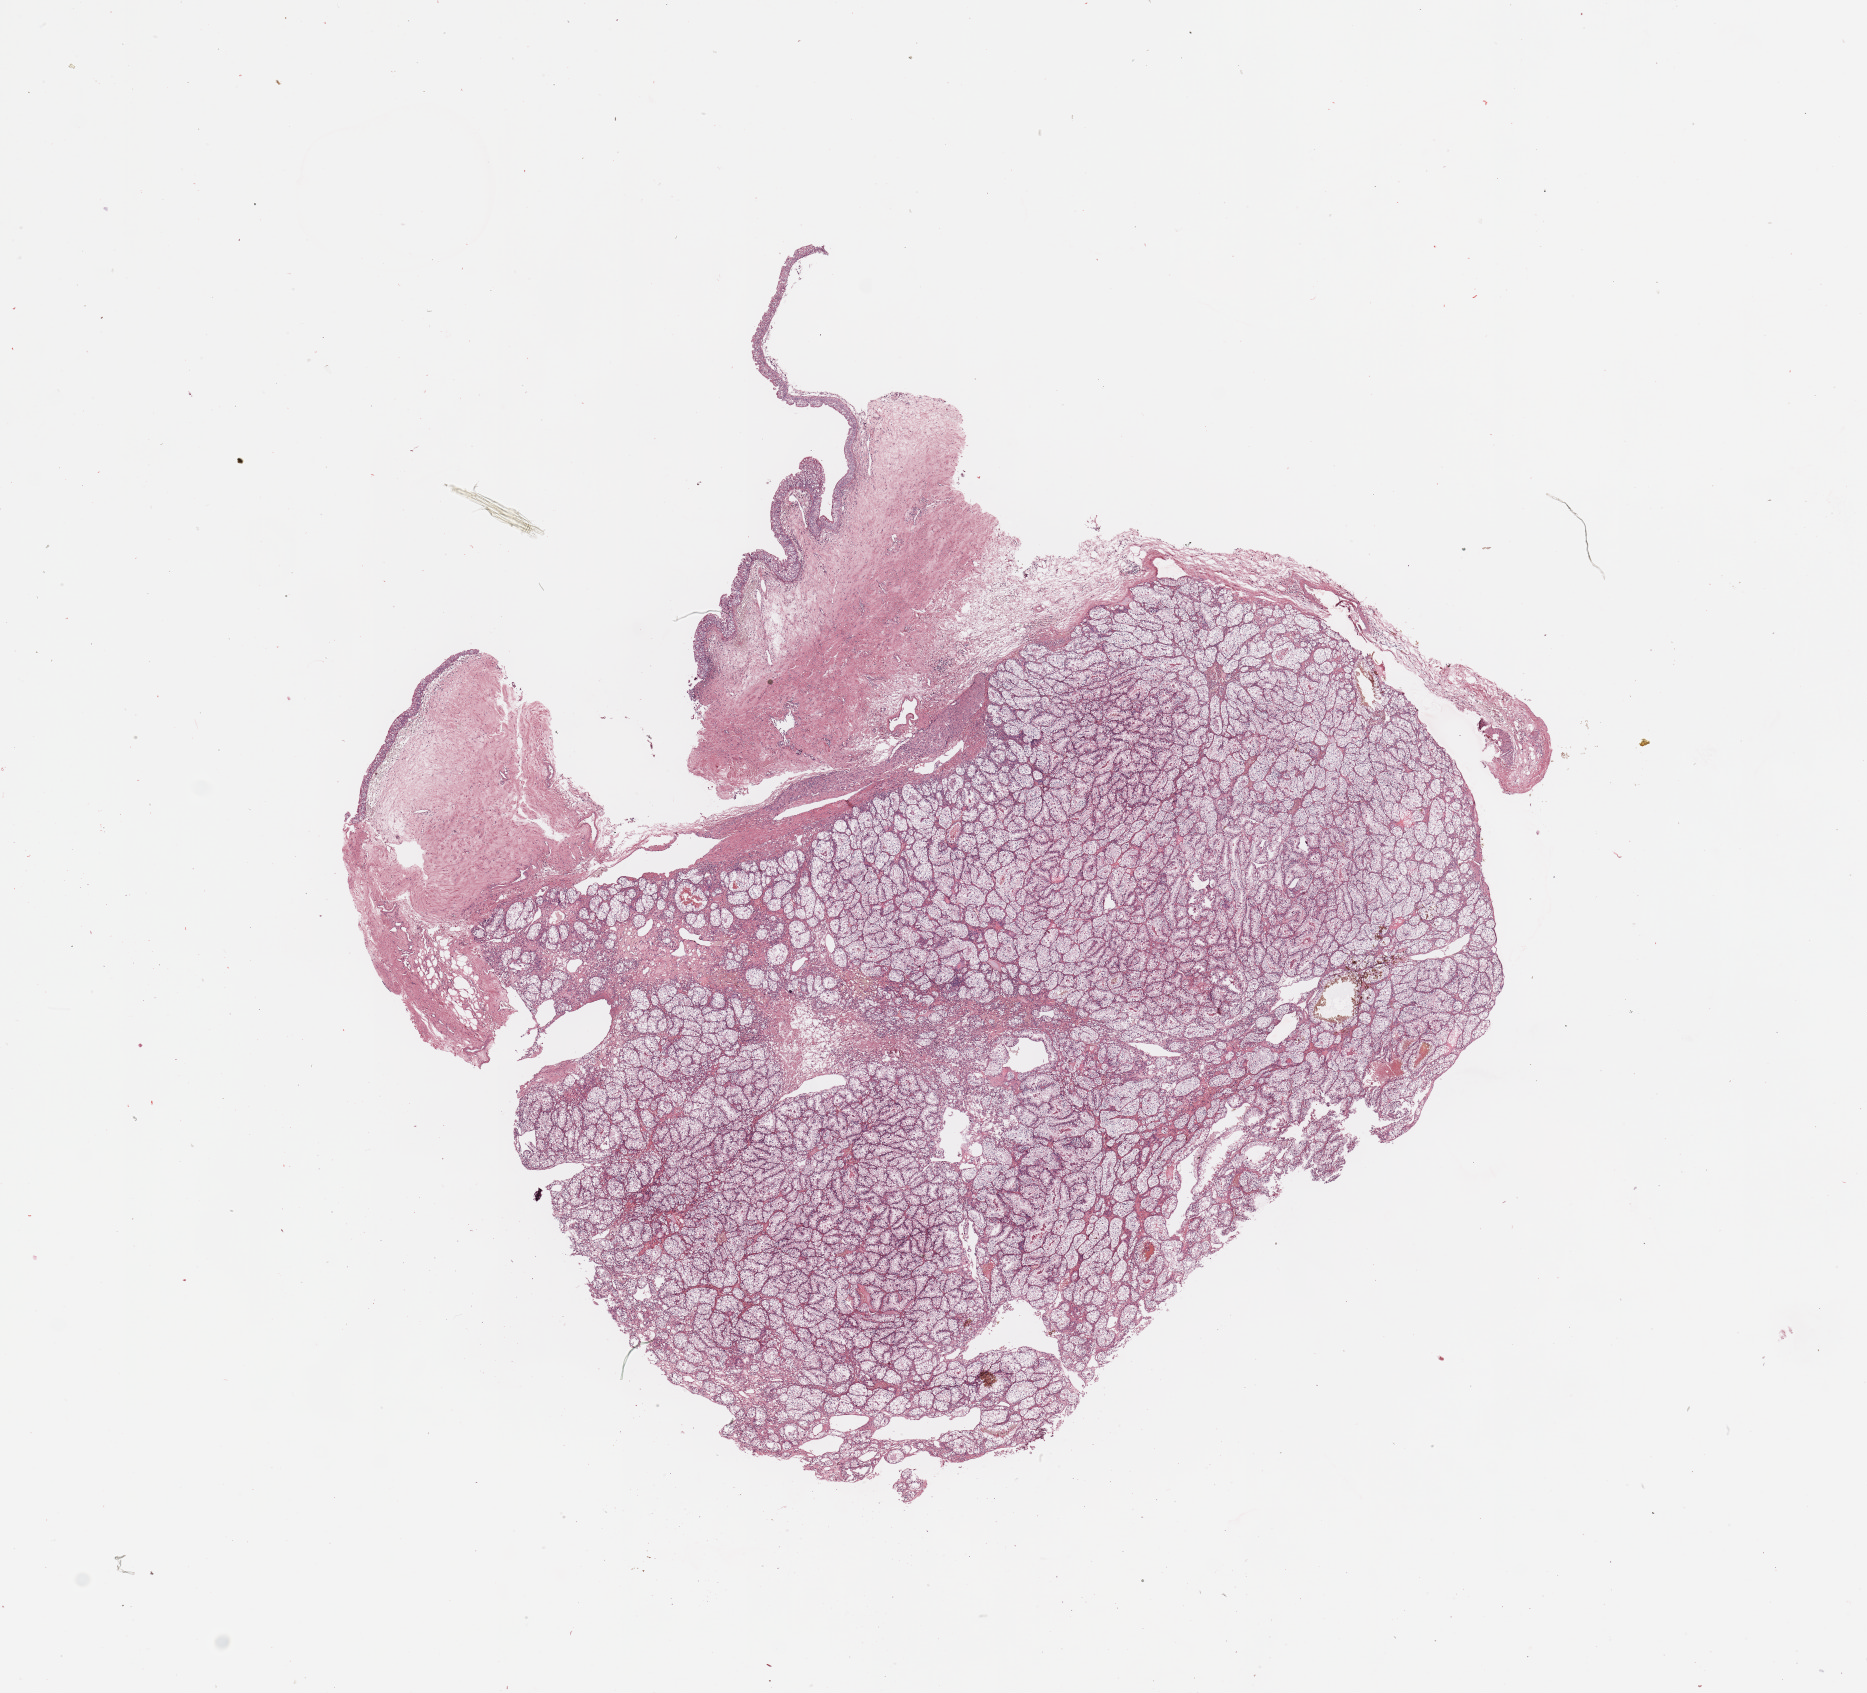
Hematoxylin and eosin (H&E) stained whole-slide image, whole scanned area (about 14.8 x 13.4 mm) shown as a low-resolution overview, tumour tissue sample, sampled site: kidney. Patient: male, age 68 years.
Histologic diagnosis: Renal cell carcinoma, NOS.